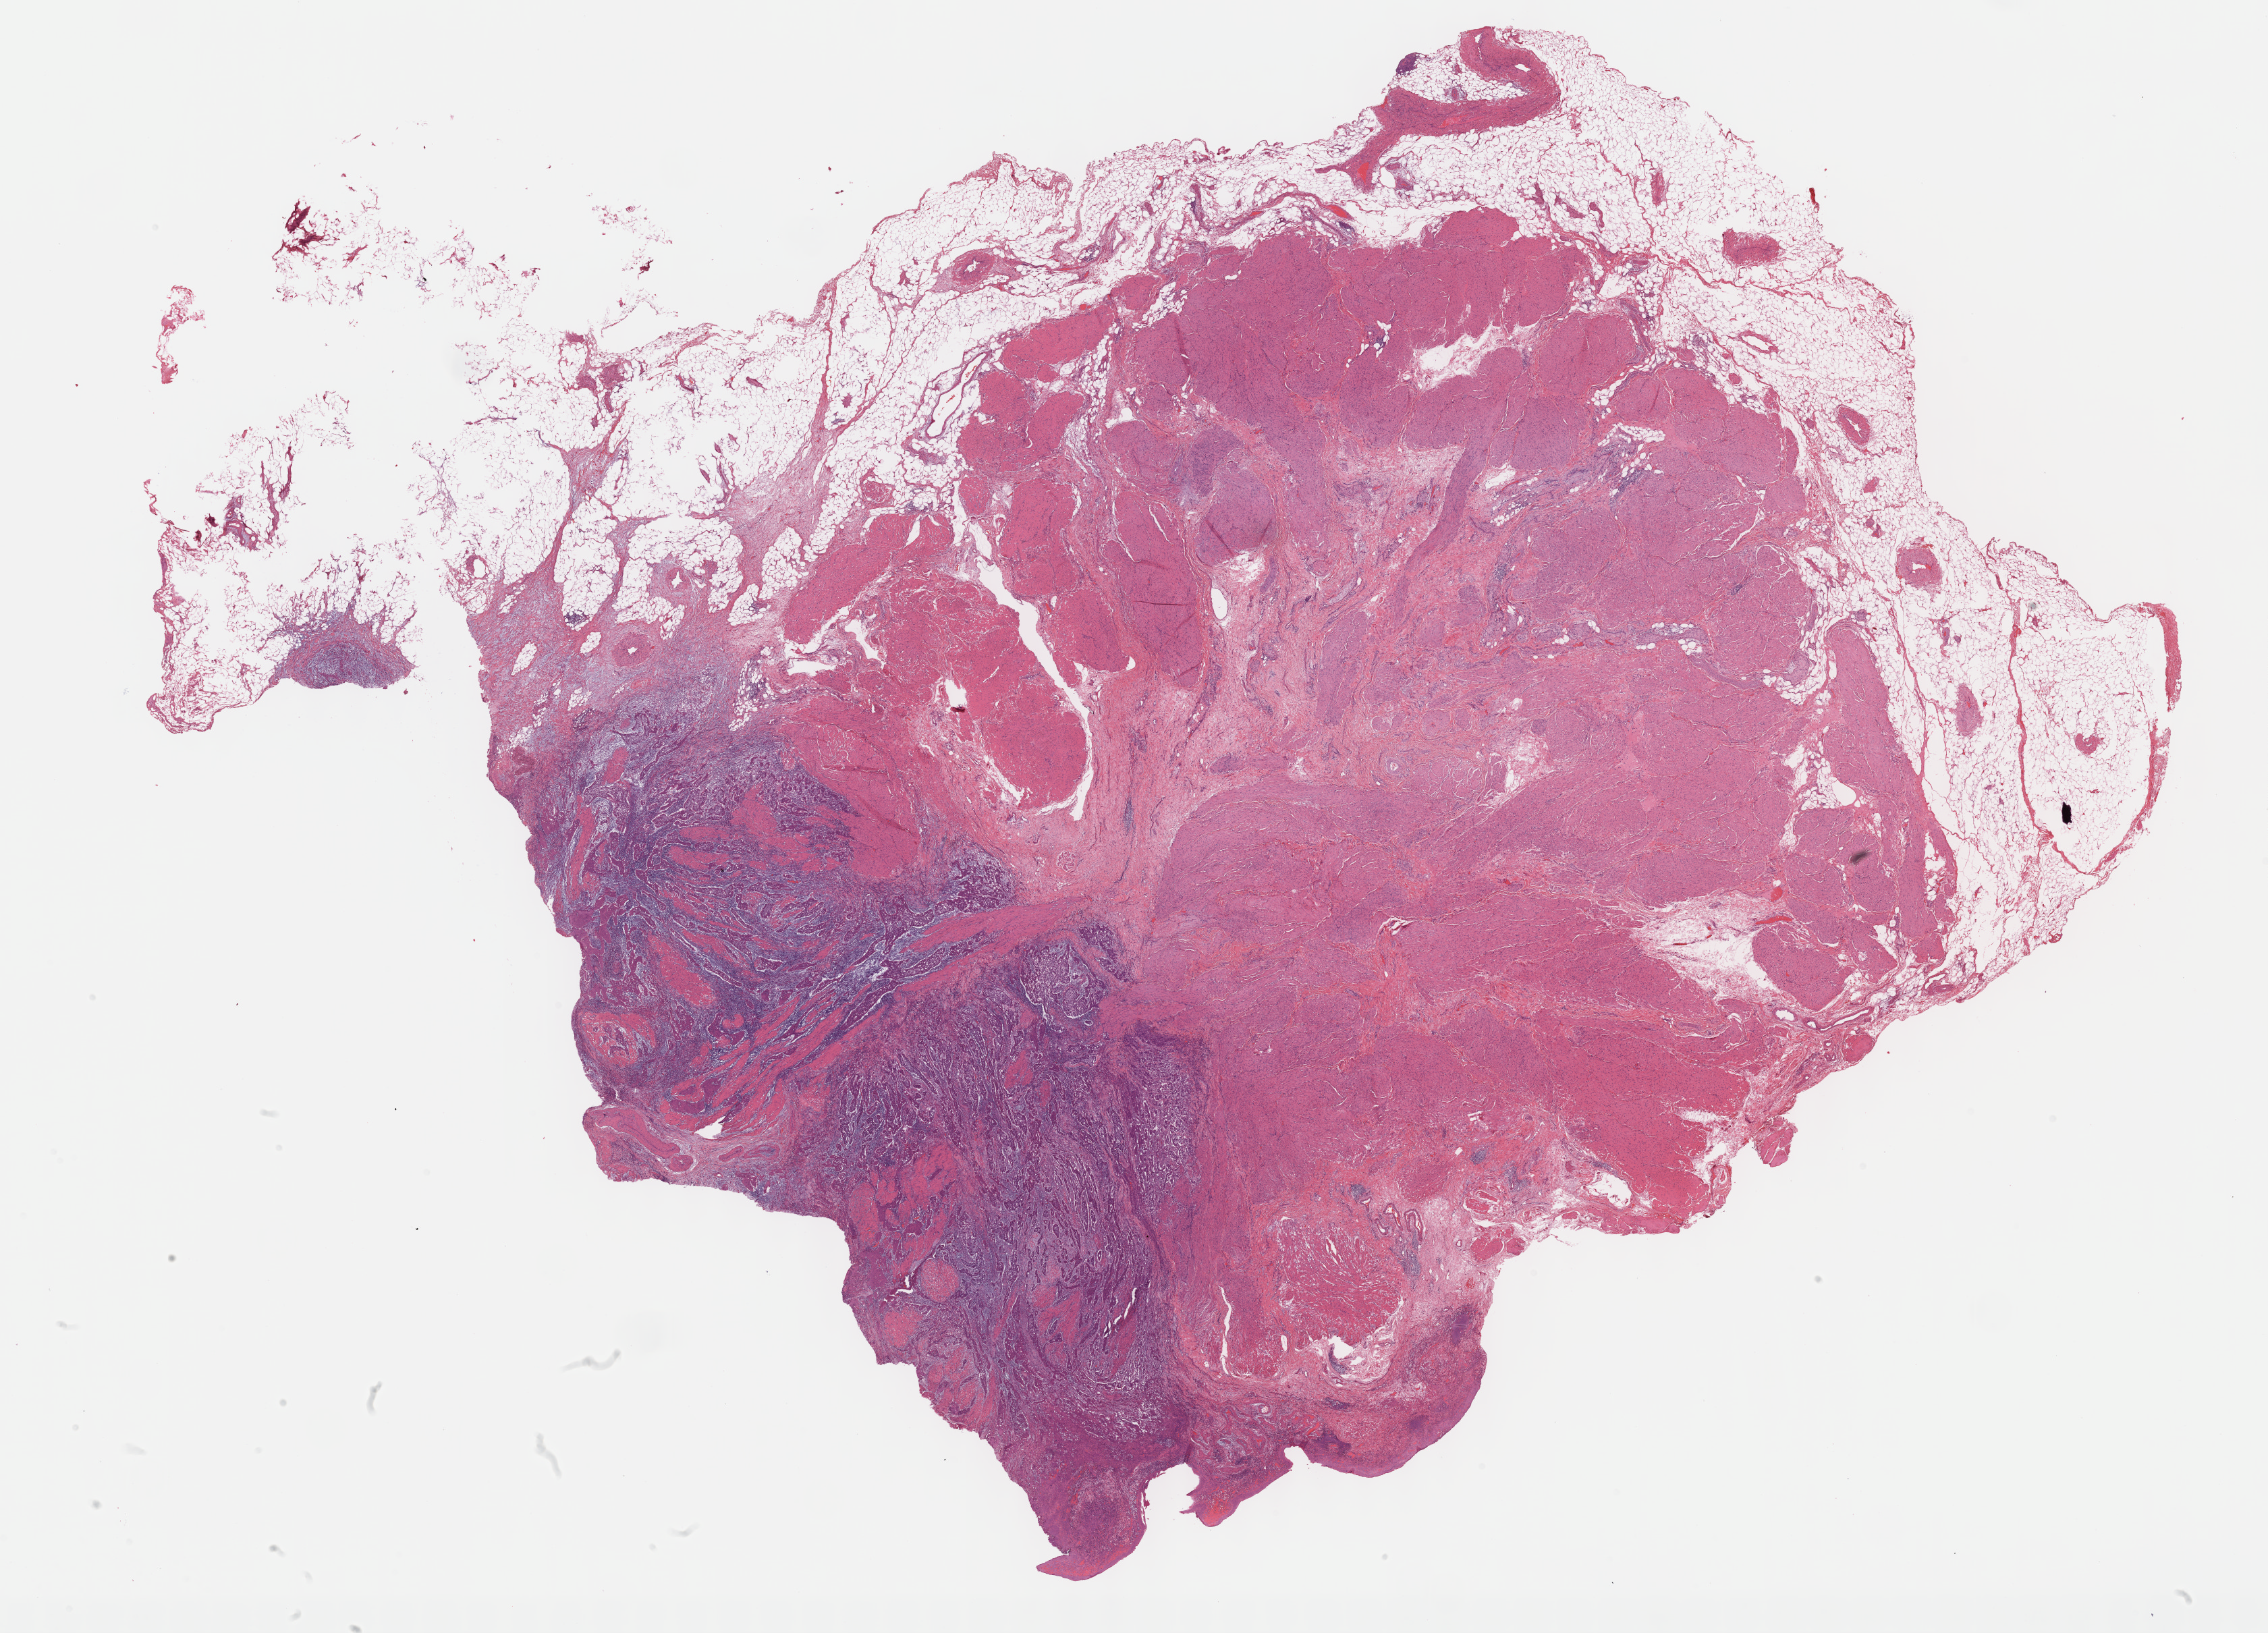
Whole-slide histology image, H&E, a low-resolution overview of the entire scanned area, about 27.2 x 19.6 mm (from a 40x scan). FFPE section. Bladder, primary tumour sample. Male, age 76 years at initial diagnosis. Histologic grade: high grade.
AJCC pathologic stage: IV (6th edition). Diagnosis: Transitional cell carcinoma. Lymph nodes positive (case pathology): 2 of 36 examined.